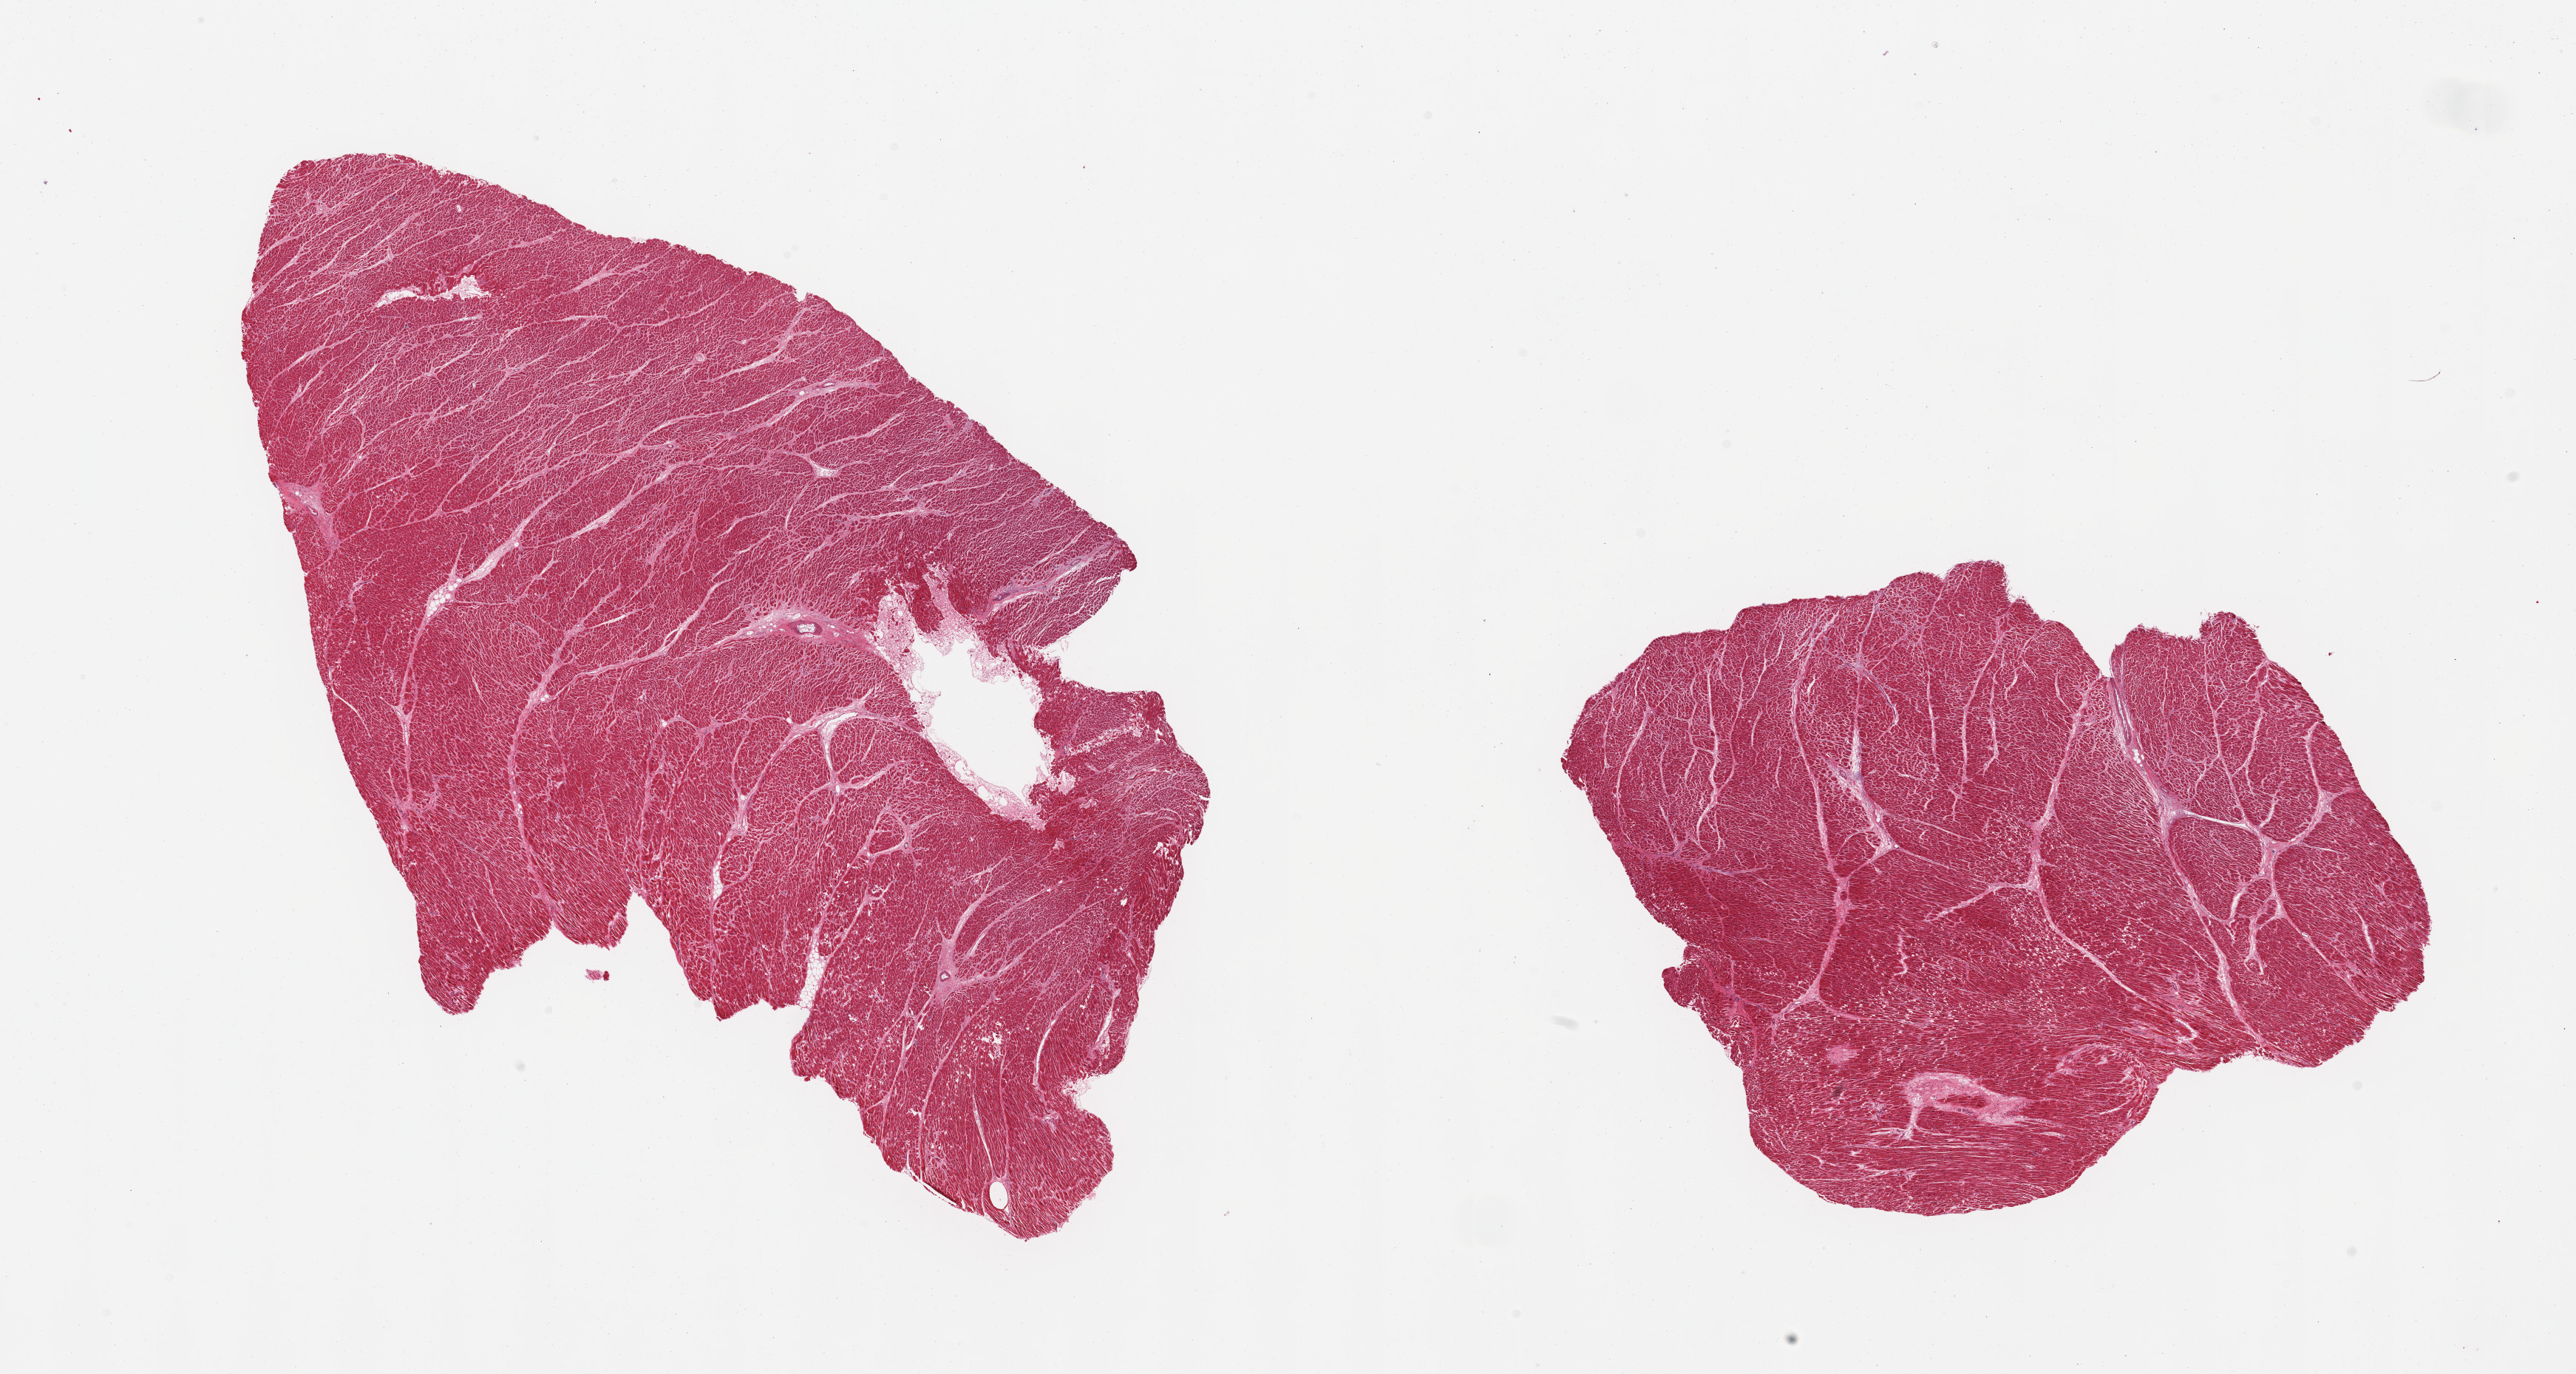
Hematoxylin and eosin (H&E) whole-slide image, a low-resolution overview of the entire scanned area, about 27.6 x 14.7 mm, PAXgene-fixed, paraffin-embedded tissue, target tissue: heart, donor tissue sample.
• reviewer comment on this tissue sample: 2 pieces